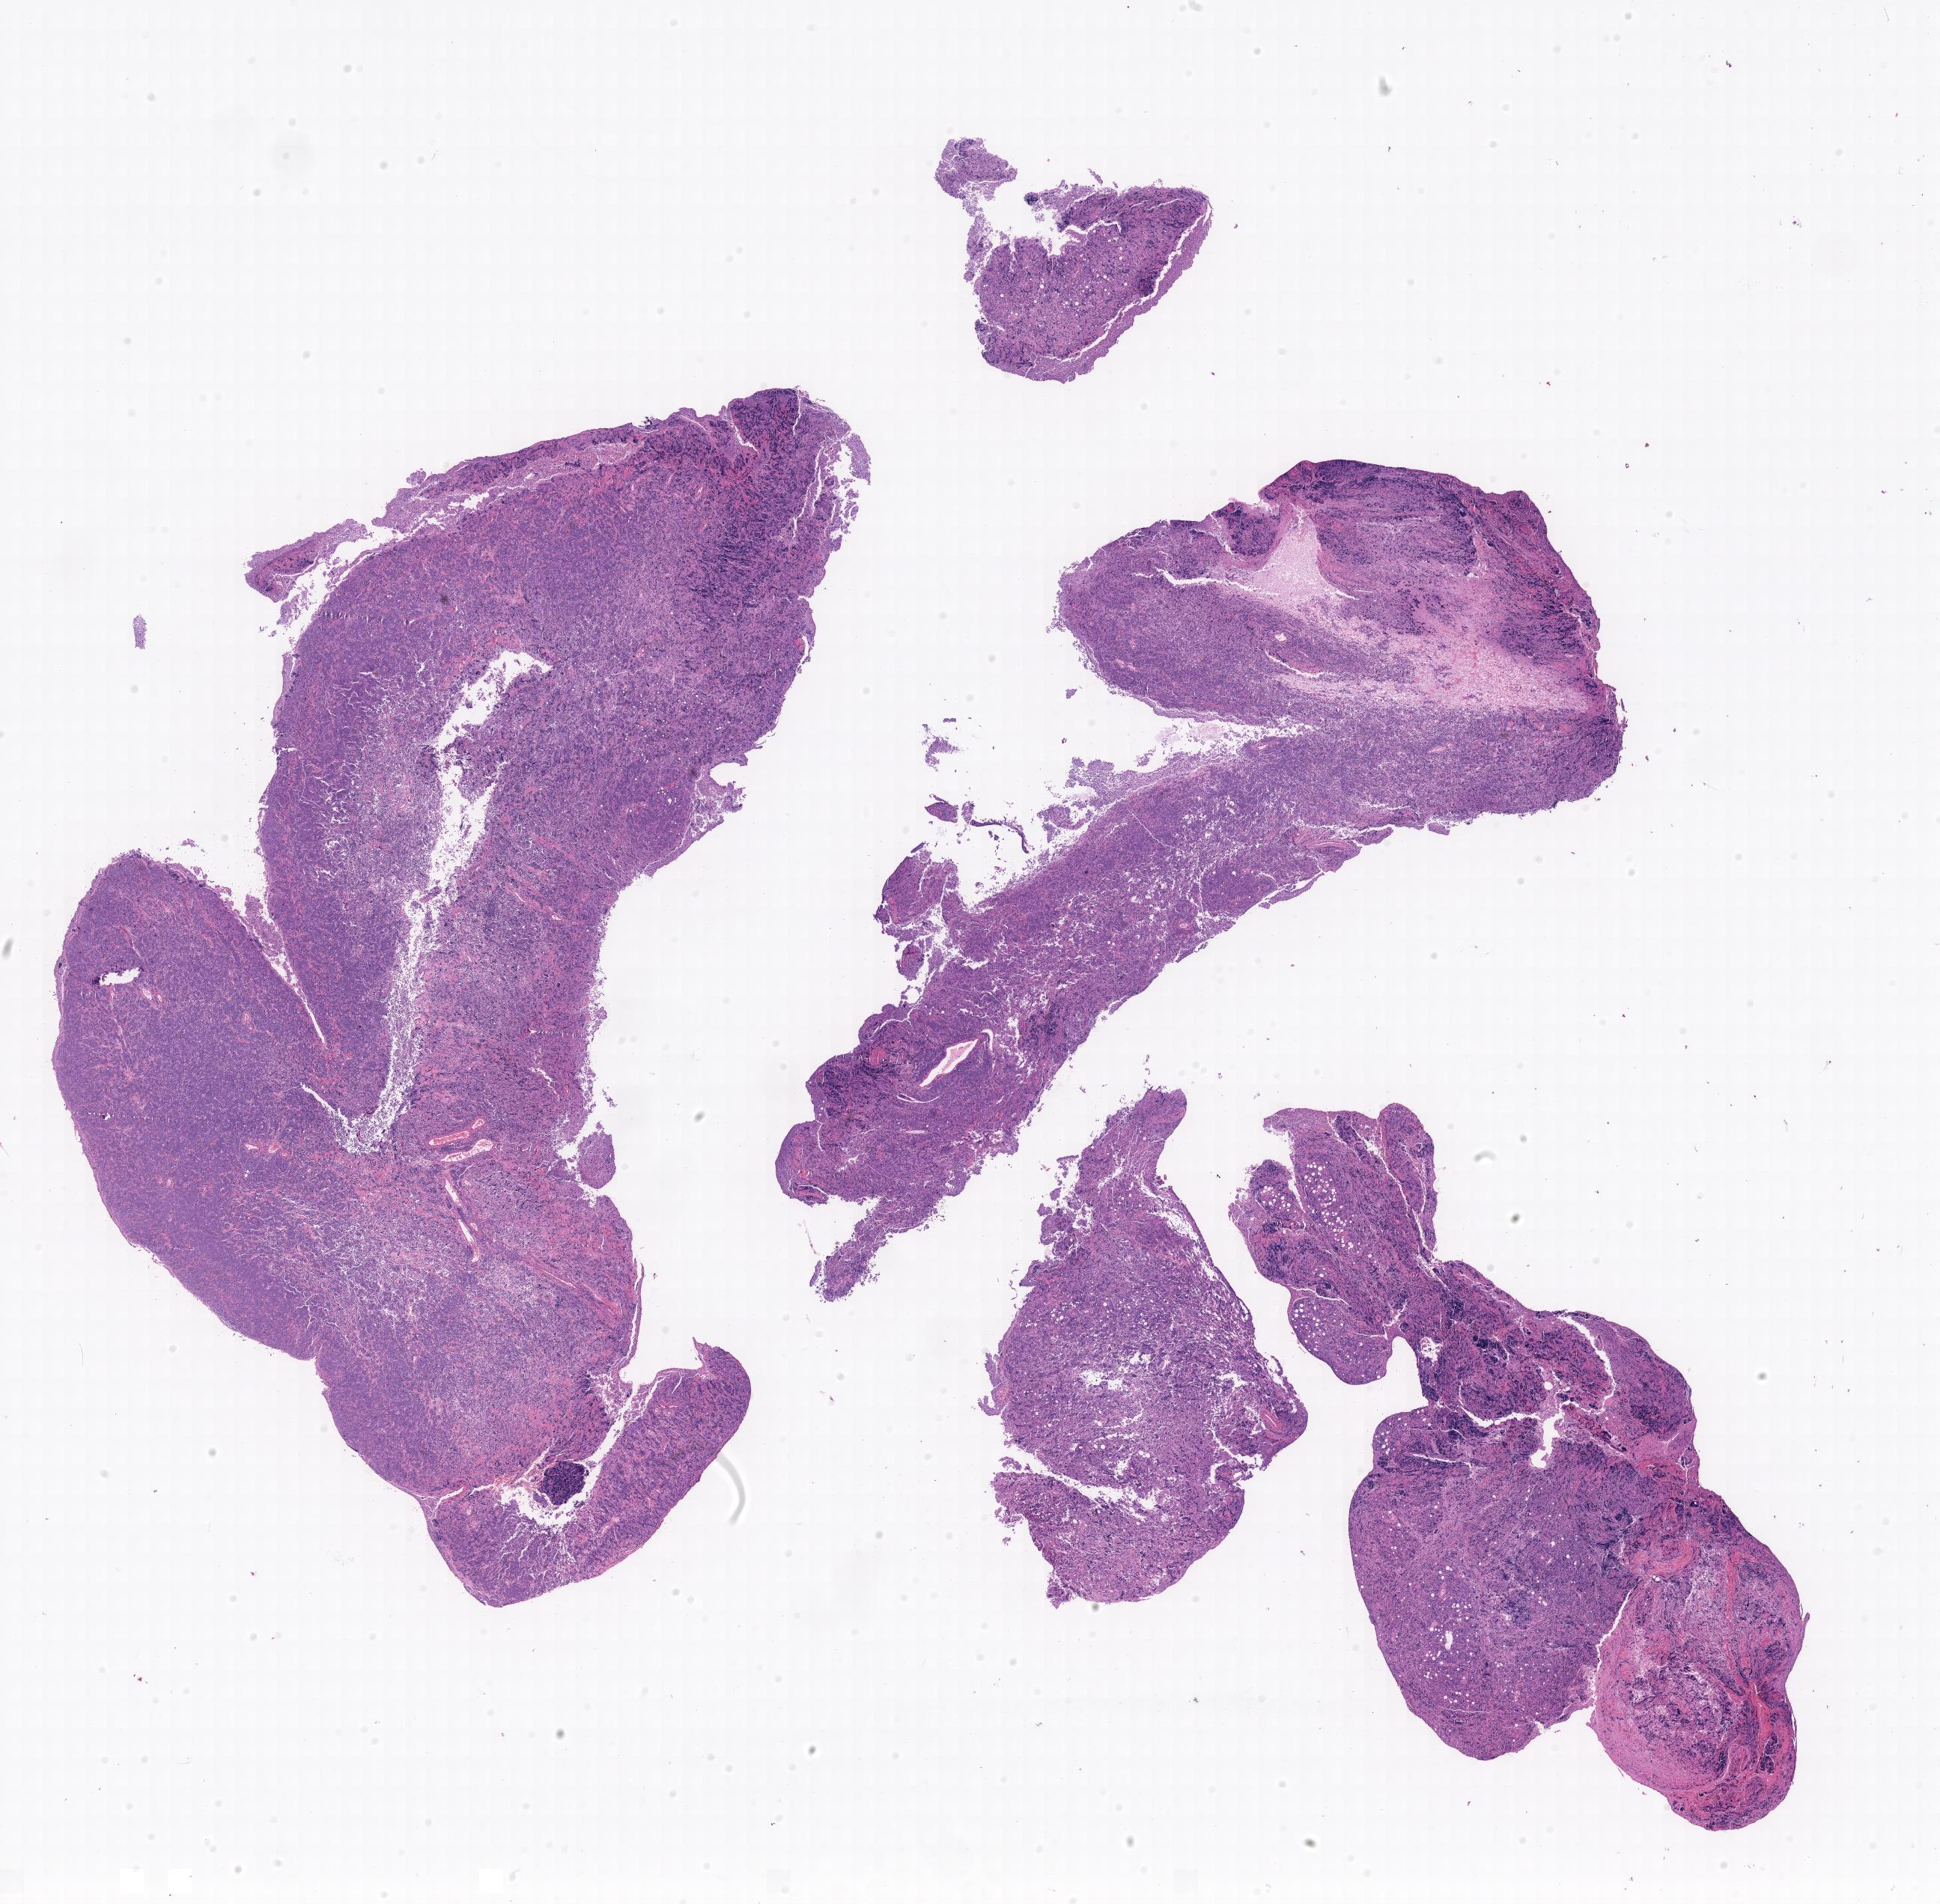
Hematoxylin and eosin (H&E) whole-slide image, shown as a low-resolution overview of the whole scanned area. Tumor tissue. Anatomic site: abdomen proper. Patient: male, age at initial diagnosis 5 years.
• histologic diagnosis: Burkitt lymphoma, NOS